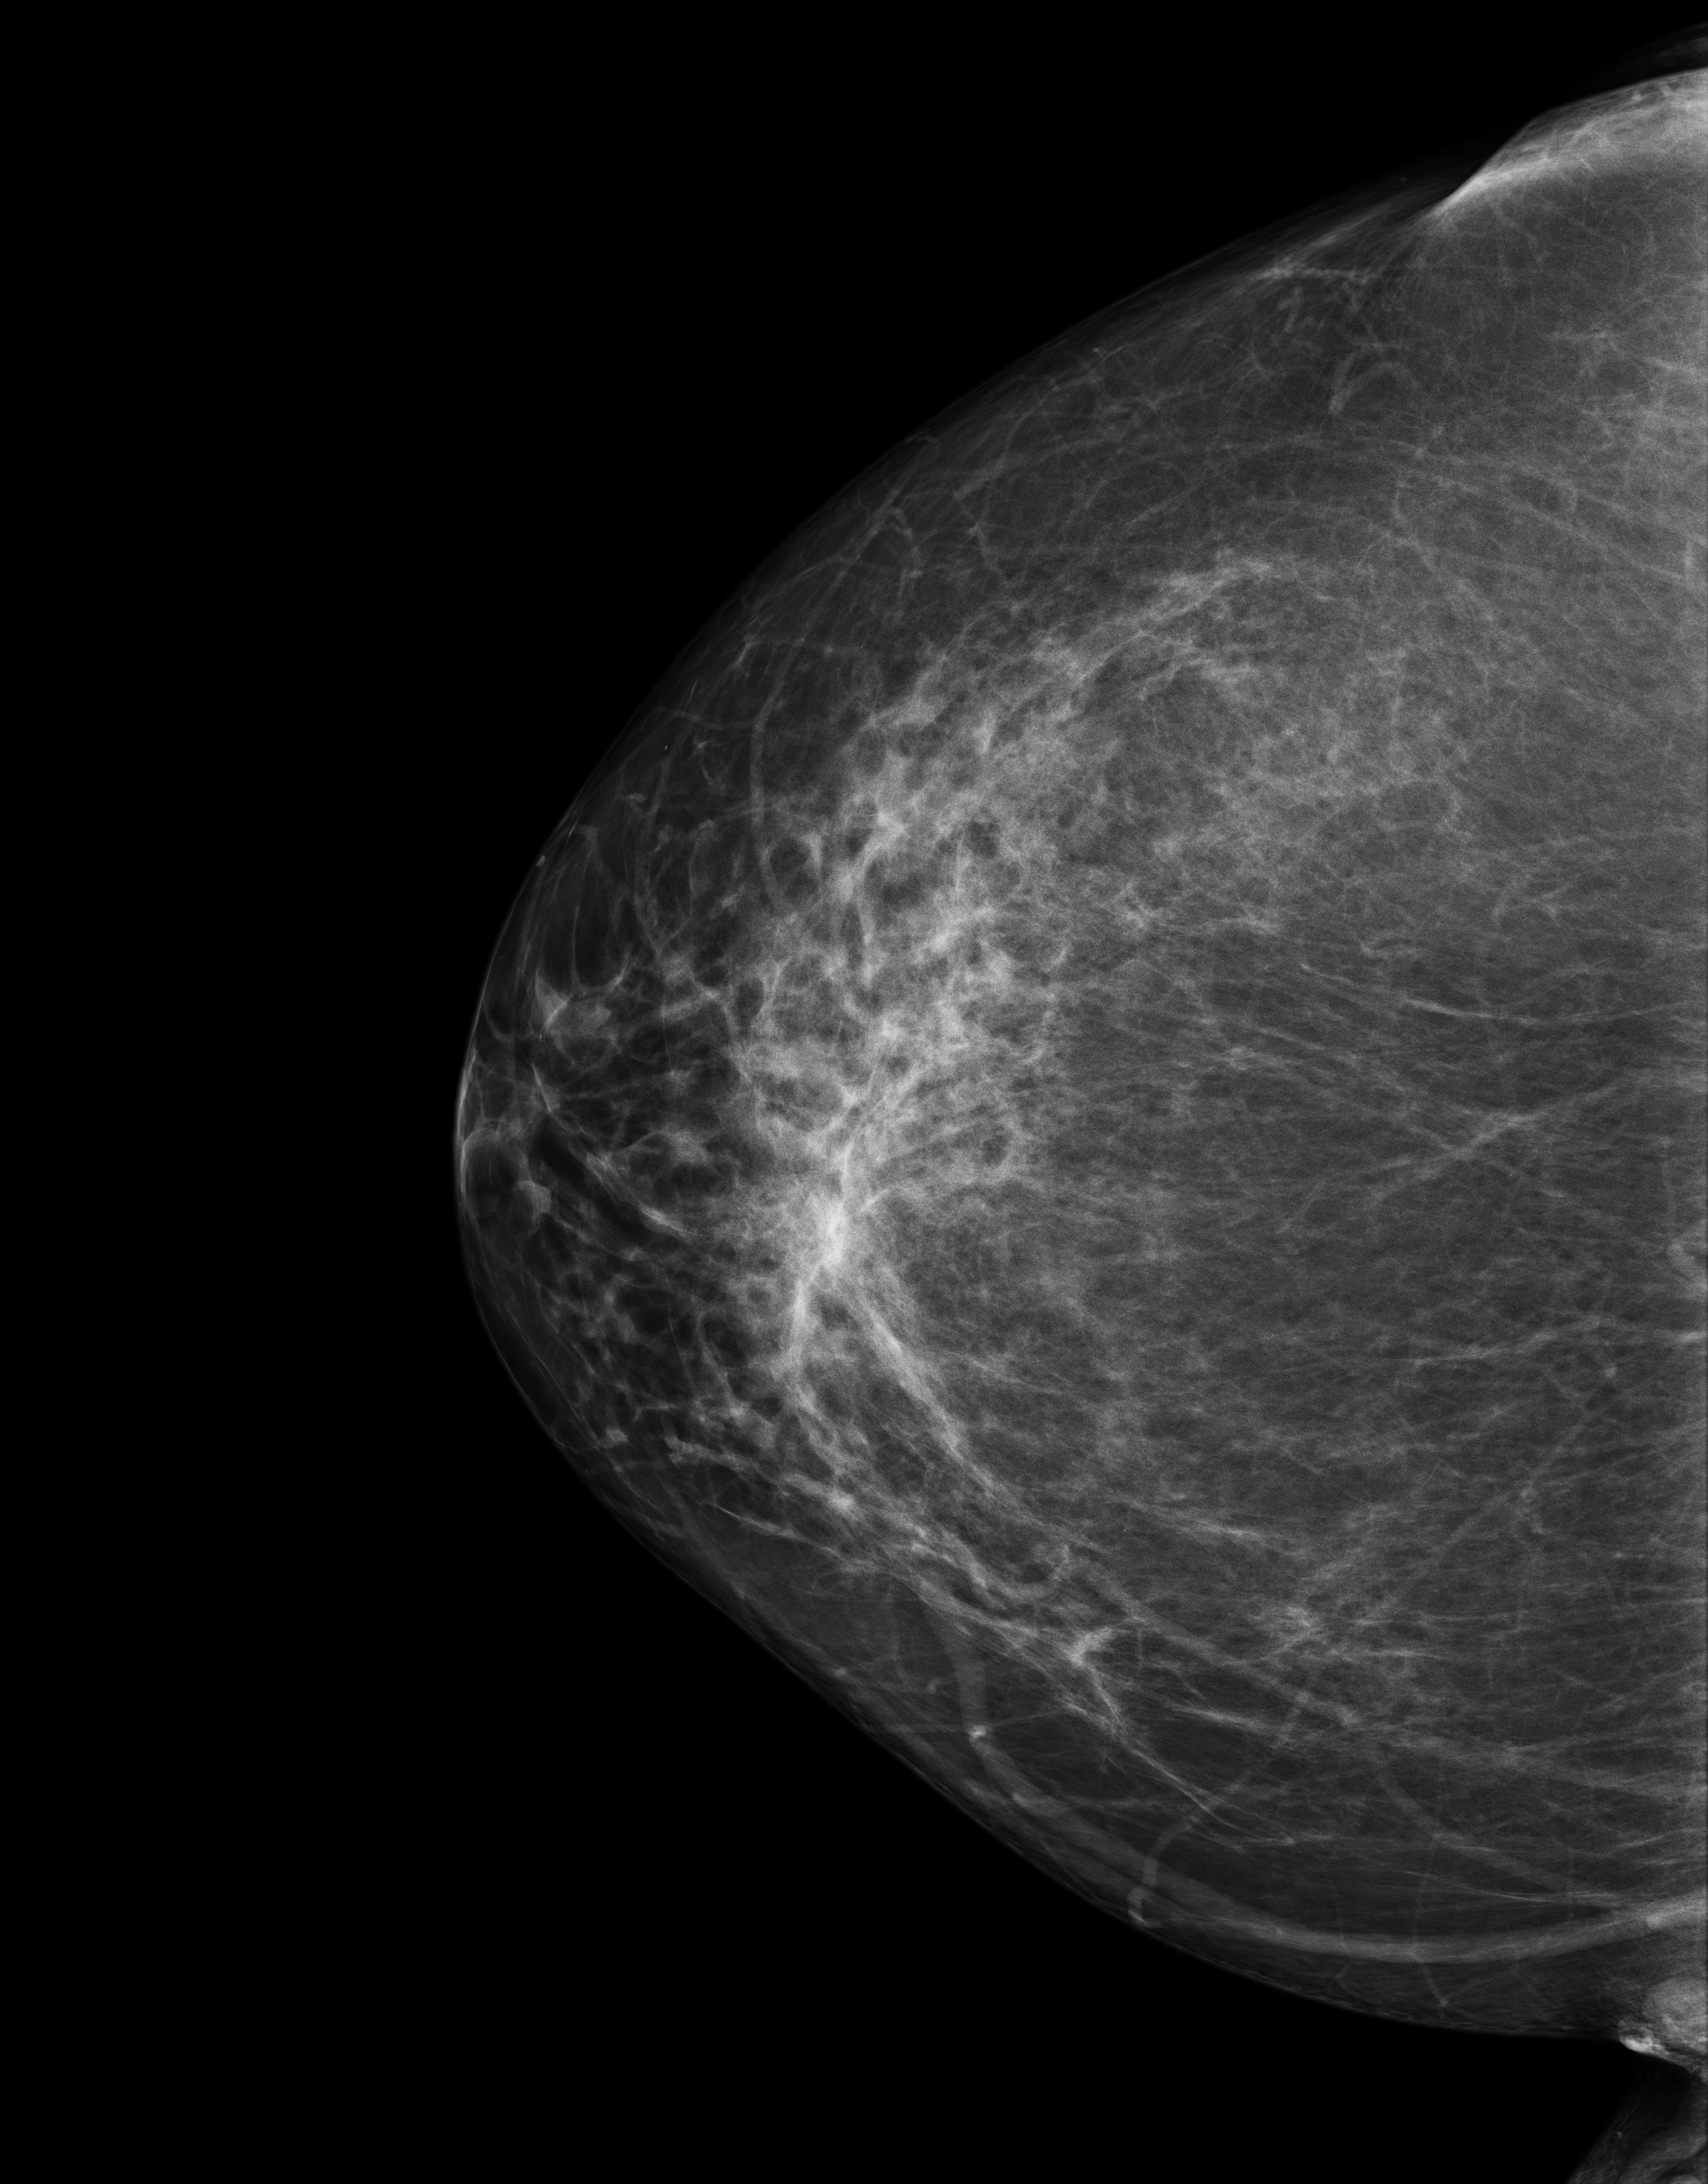
Annual screening mammography examination; system: Senographe Essential ADS_56.21.3. Patient aged 58 years (female).
Image type: full-field digital mammogram. Breast: right. Projection: craniocaudal (CC) view.